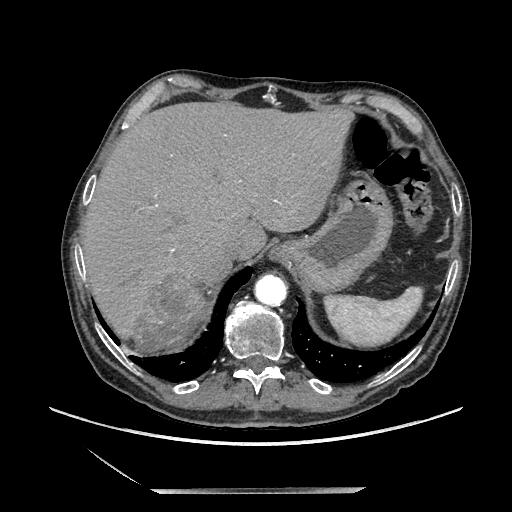
Contrast-enhanced abdominal CT, one axial slice; position 173 of 243 along the scan axis; soft-tissue window (W 400 / L 40 HU); 512 × 512 image matrix, field of view 420 × 420 mm. Male patient. From the clinical record (not read from this slice): diagnosis: adrenocortical carcinoma; tumour side: right adrenal; tumour size at pathology: 16 cm; Ki-67 index: 17 %; stage (as recorded): 3.
Outlined on this slice (semi-automatic segmentation, software-assisted and operator-edited):
- mass: bounding box [x1, y1, x2, y2] px = [130, 276, 202, 353]